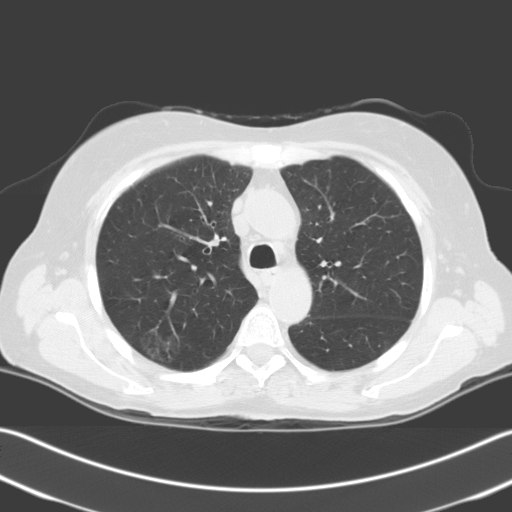
Axial slice from a low-dose chest CT screening exam, first (baseline) screen, lung window (W 1500 / L -600 HU), 3.2 mm slice thickness, standard (soft-tissue) reconstruction kernel (C), 140 kVp, slice 52 of 204 in the series, 512 × 512 image matrix. Female participant, aged 67 years at enrolment. Current smoker at enrolment.
- Lesion marked by an expert reader, box from (x=125, y=325) to (x=186, y=373) px.
- The screening reader recorded 2 non-calcified nodules or masses ≥4 mm on this exam (right upper lobe, right upper lobe); which of them this box marks is not recorded.
- Official screen result: positive, change unspecified: nodule(s) >= 4 mm or enlarging nodule(s), mass(es), or other non-specific abnormalities suspicious for lung cancer.
- Lung cancer was diagnosed 24 days after this screen: squamous cell carcinoma, NOS, right upper lobe, stage IIIA (AJCC 6th edition), 56 mm at pathology.